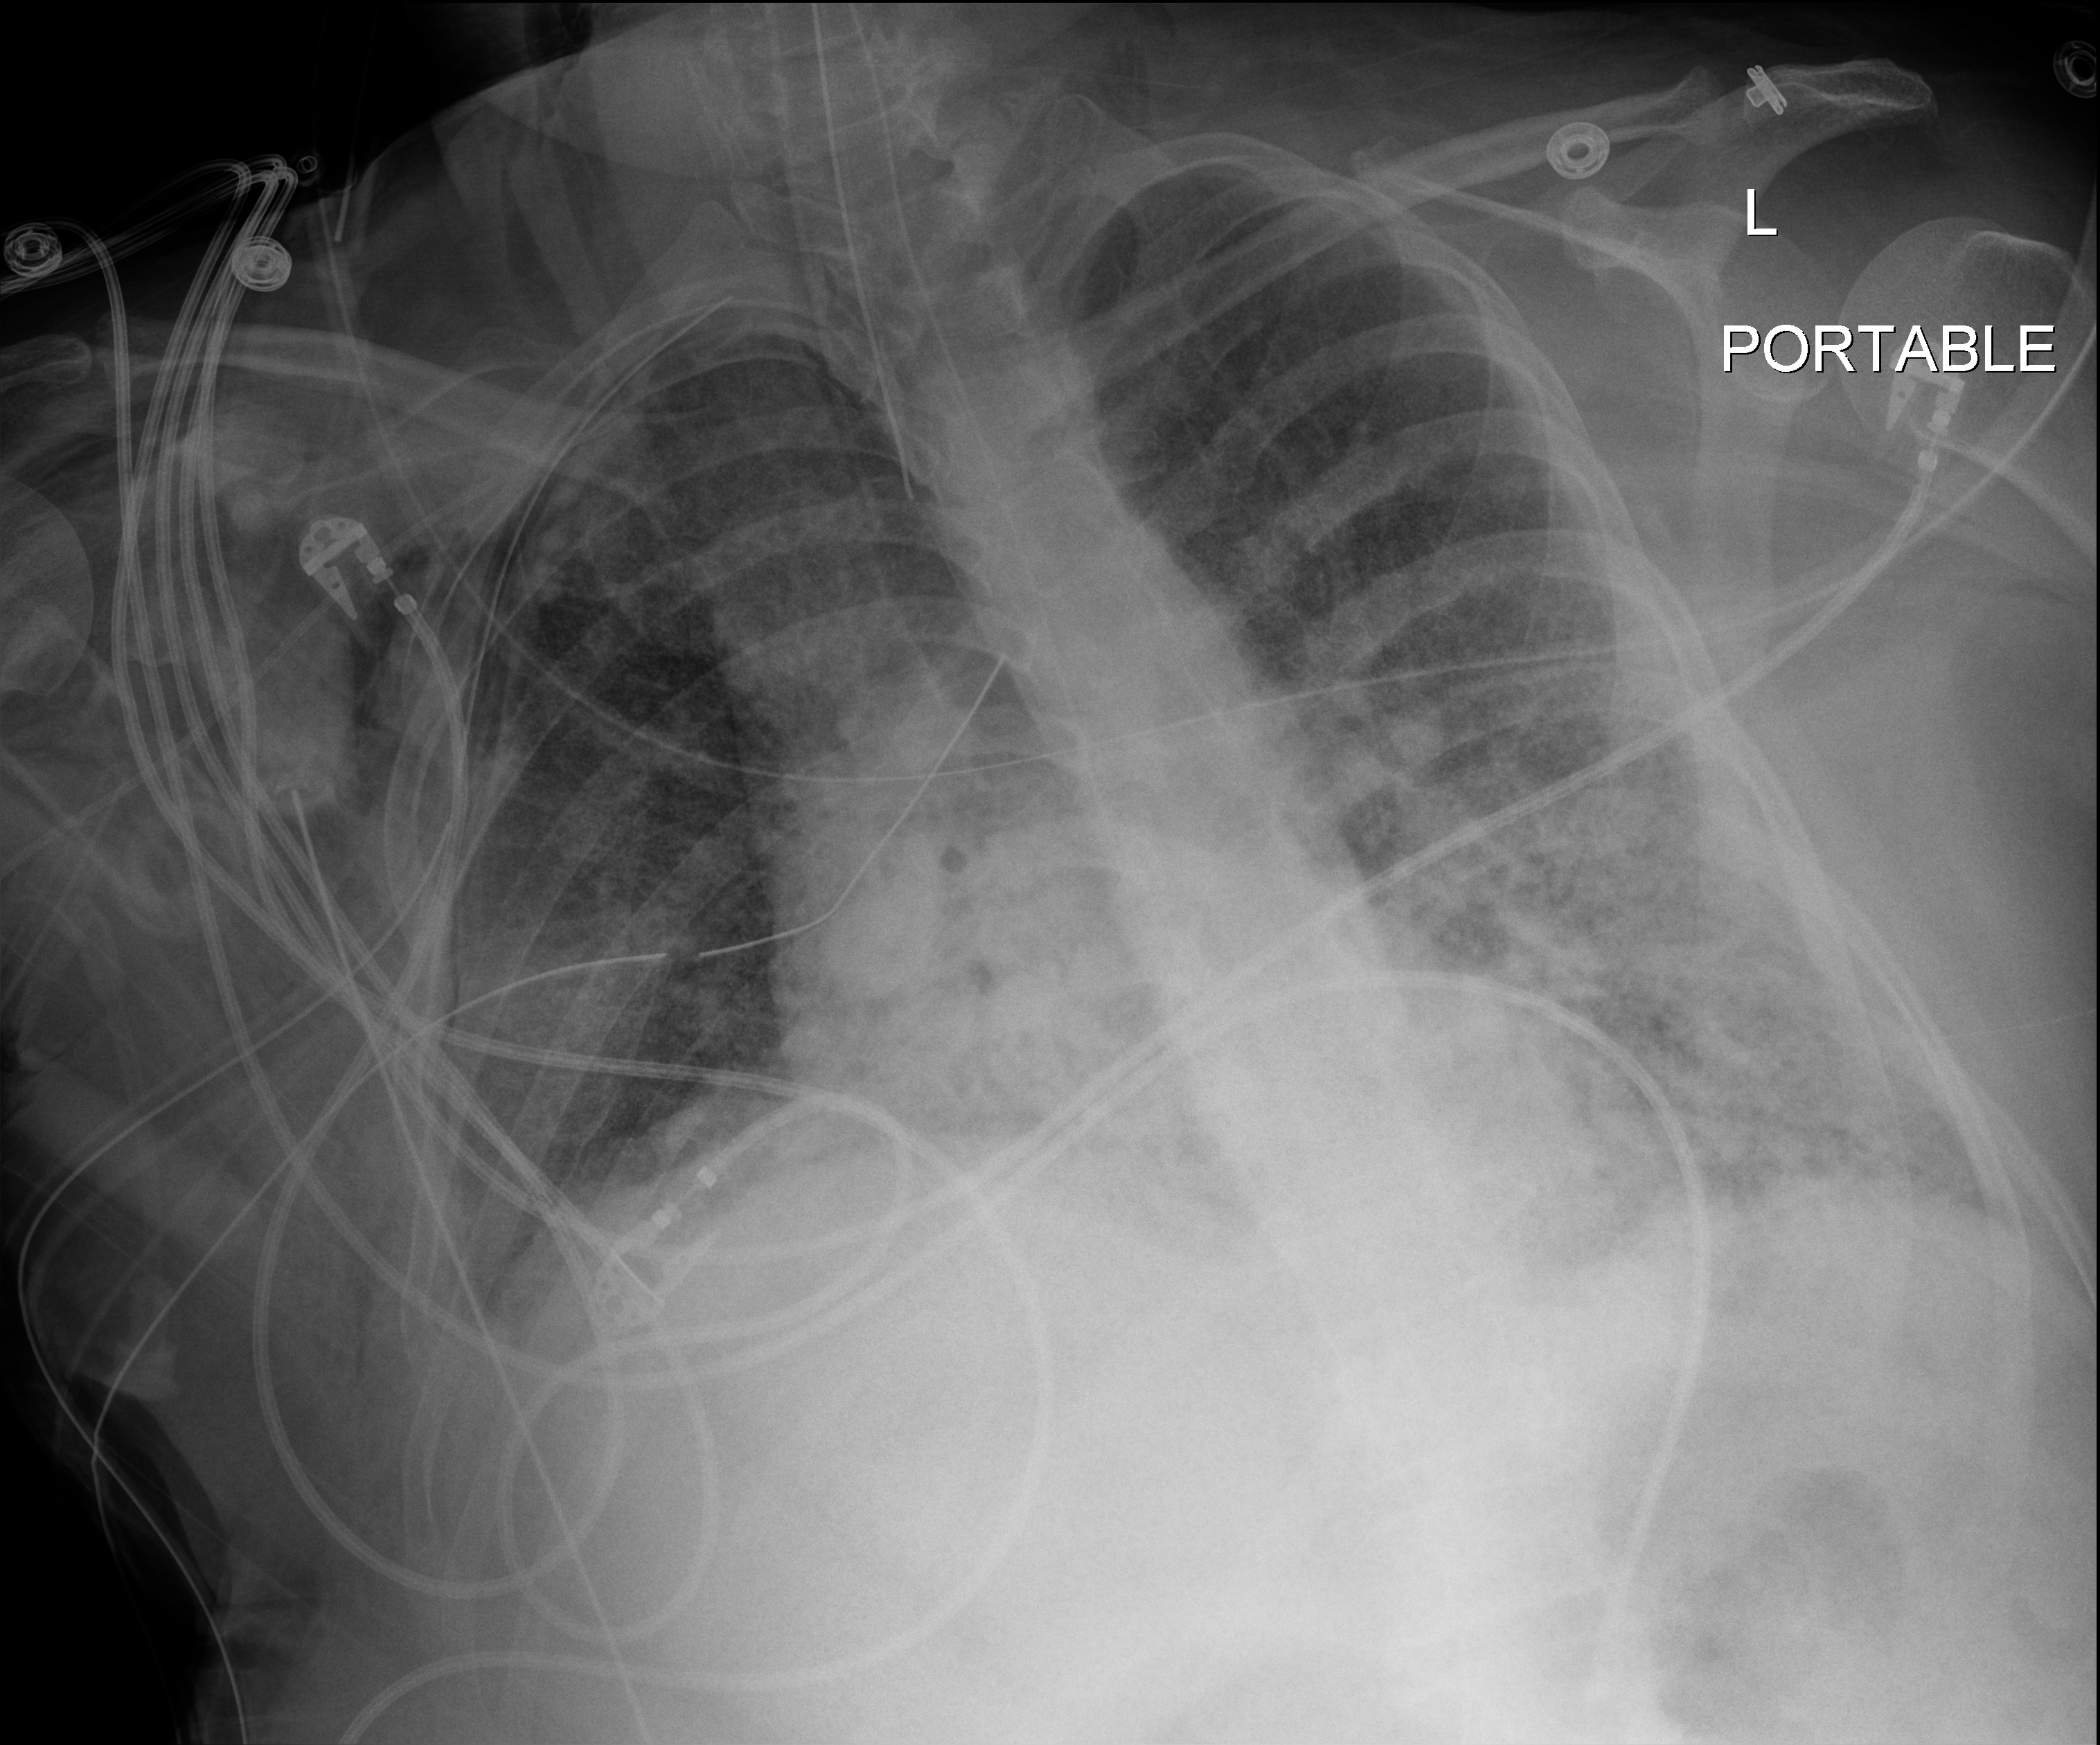
Bedside chest radiograph (digital radiography); anteroposterior (AP) projection. Patient hospitalised with COVID-19, aged 18–59 years.
From the hospital-stay record, not from the radiograph (when in the stay this image was taken is not recorded):
- COPD (admission record): no
- diabetes (admission record): no
- mechanically ventilated during this hospital stay: yes